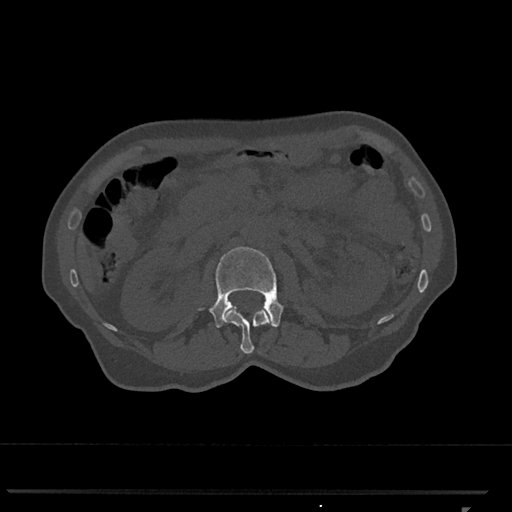
CT including the spine, one axial slice. Slice 364 of 793 in the series (ordered by position). Reconstruction kernel Br40s/3. 120 kVp. Bone window (W 1800 / L 400 HU). 512 × 512 image matrix, field of view 380 × 380 mm. Female patient, age 62 years. Case-level facts recorded for this patient, not image findings: primary cancer: renal.
Annotated regions visible in this slice (semi-automatic segmentation, software-assisted and operator-edited):
- L1 vertebra: bounding box [x1, y1, x2, y2] px = [223, 308, 272, 354]
- L2 vertebra: [200, 247, 283, 328]